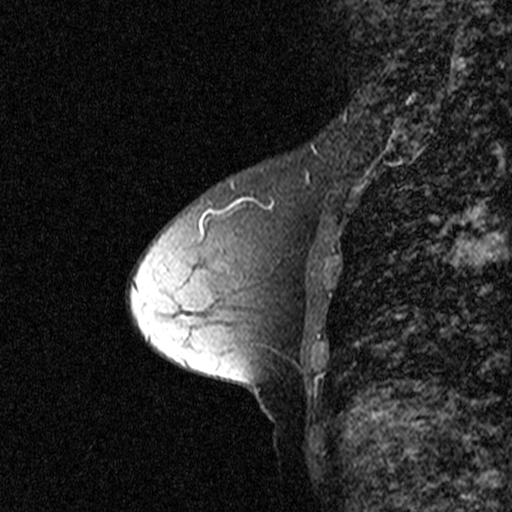
Breast MRI (dynamic contrast-enhanced), one sagittal slice. Position 20 of 44 along the scan axis. Dynamic contrast-enhanced study with each time point stored as its own series, time point 2 of 3 at this slice position (early post-contrast, ordered by acquisition time). 1.5 T. TE 4.5 ms, TR 11 ms. 512 × 512 image matrix, field of view 200 × 200 mm. Female patient, age 53 years. Case-level facts recorded for this patient, not image findings: setting: breast cancer imaged before/during neoadjuvant chemotherapy; receptor status: HR-positive, HER2-negative.
Annotated regions visible in this slice (semi-automatically segmented with operator editing):
- analysis volume of interest (the breast-tissue region the enhancement analysis was run in; not a lesion): box from (x=200, y=178) to (x=317, y=309) px
- tumour enhancement mask (voxels above the 90 % enhancement threshold inside the analysis volume of interest): (x=248, y=198)–(x=273, y=209)